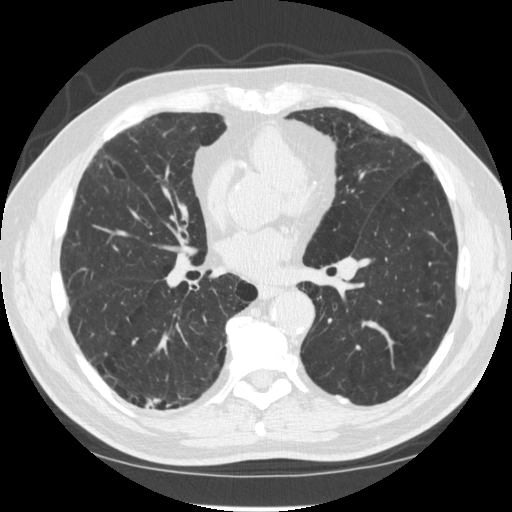
Chest CT (low-dose screening protocol), one axial image, second annual screen, lung window (W 1500 / L -600 HU), 1.25 mm slice thickness, 512 × 512 image matrix, field of view 360 × 360 mm. Male, age 70 years at enrolment. Former smoker at enrolment.
- Lesion marked by an expert reader, bounding box <132,379,183,429> (left, top, right, bottom; pixels).
- The screening reader recorded 2 non-calcified nodules or masses ≥4 mm on this exam (right lower lobe, right lower lobe); which of them this box marks is not recorded.
- Participant outcome: lung cancer diagnosed 617 days after this screen (after the third annual screen) — squamous cell carcinoma, NOS, right upper lobe, poorly differentiated (G3), stage IV (AJCC 6th edition).